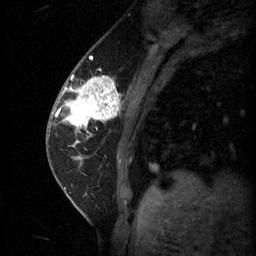
Breast MRI (dynamic contrast-enhanced), one sagittal slice; slice 17 of 60 in the series (ordered by position); 3 images stored at this slice position (order not interpretable as contrast timing); 1.5 T; TE 4.2 ms, TR 11 ms; 256 × 256 image matrix, field of view 180 × 180 mm. Patient: female, 62 years.
Structures marked on this image (semi-automatically segmented with operator editing):
- analysis volume of interest (the breast-tissue region the enhancement analysis was run in; not a lesion): bounding box <55,72,123,135> (left, top, right, bottom; pixels)
- tumour enhancement mask (voxels above the 70 % enhancement threshold inside the analysis volume of interest): <58,76,121,129>